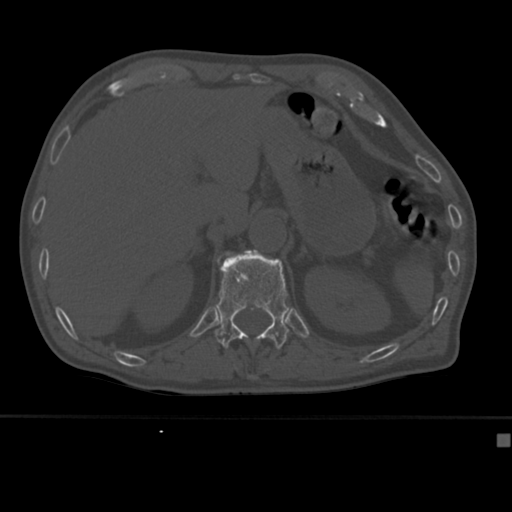
CT including the spine, one axial slice; slice 192 of 430 in the series (ordered by position); reconstruction kernel Br40s; bone window (W 1800 / L 400 HU); 1.5 mm slice thickness; 512 × 512 image matrix, field of view 337 × 337 mm. Male patient, age 64 years. From the clinical record (not read from this slice): primary cancer: uterus.
Structures marked on this image (semi-automatic segmentation, software-assisted and operator-edited):
- L1 vertebra: box from (x=217, y=255) to (x=223, y=263) px
- T11 vertebra: (x=251, y=376)–(x=254, y=378)
- T12 vertebra: (x=215, y=250)–(x=289, y=349)